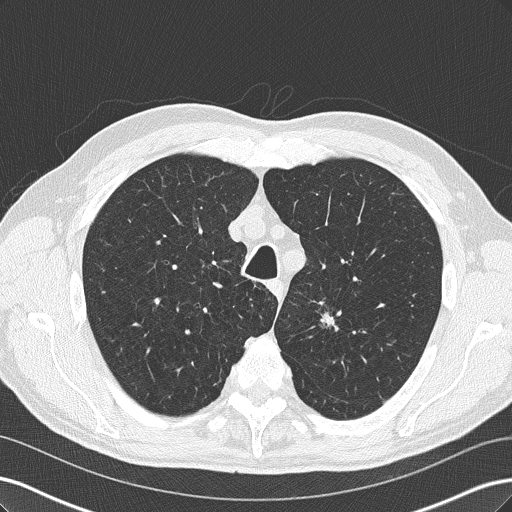
Axial slice from a low-dose chest CT screening exam. Third screening round (two years after baseline). Lung window (W 1500 / L -600 HU). 2 mm slice thickness. Male, age 66 years at enrolment.
Expert reader's lesion annotation, box from (x=300, y=301) to (x=351, y=347) px. The exam's reader record, not a measurement of the box and not confirmed to be the same lesion: non-calcified nodule or mass ≥4 mm, left upper lobe, 14 × 9 mm, spiculated (stellate) margins, soft tissue attenuation, pre-existing on the prior screen: yes; interval growth: yes. Official screen result: positive, other.